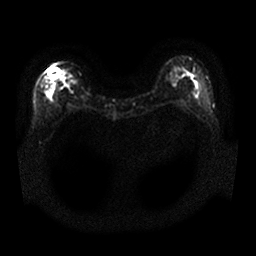
Breast MRI, one axial slice. Diffusion-weighted series; image 2 of 4 stored at this slice position (different b-values; order by instance number). 1.5 T. 4 mm slice thickness. 256 × 256 image matrix, field of view 340 × 340 mm. Female patient.
Structures marked on this image (outlined manually by an expert reader):
- tumour on diffusion-weighted imaging: bounding box [x1, y1, x2, y2] px = [48, 67, 61, 80]